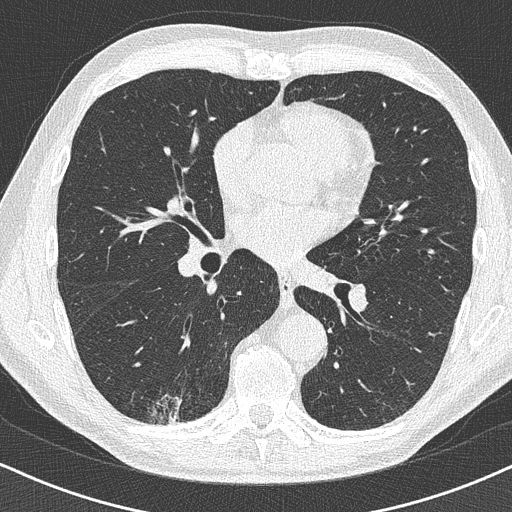
Axial slice from a low-dose chest CT screening exam. Baseline annual screen. Lung window (W 1500 / L -600 HU). 1 mm slice thickness. Slice 219 of 438 in the series. 512 × 512 image matrix, field of view 320 × 320 mm. Male, age 63 years at enrolment.
Expert reader's lesion annotation, bounding box <131,364,203,429> (left, top, right, bottom; pixels). Screening reader's record for this exam (one nodule recorded; not confirmed to be the boxed lesion): non-calcified nodule or mass ≥4 mm, right lower lobe, 16 × 13 mm, poorly defined margins. Later outcome: lung cancer diagnosed 74 days after this screen — adenocarcinoma, NOS, right lower lobe, moderately differentiated (G2), stage IA (AJCC 6th edition), 20 mm at pathology.